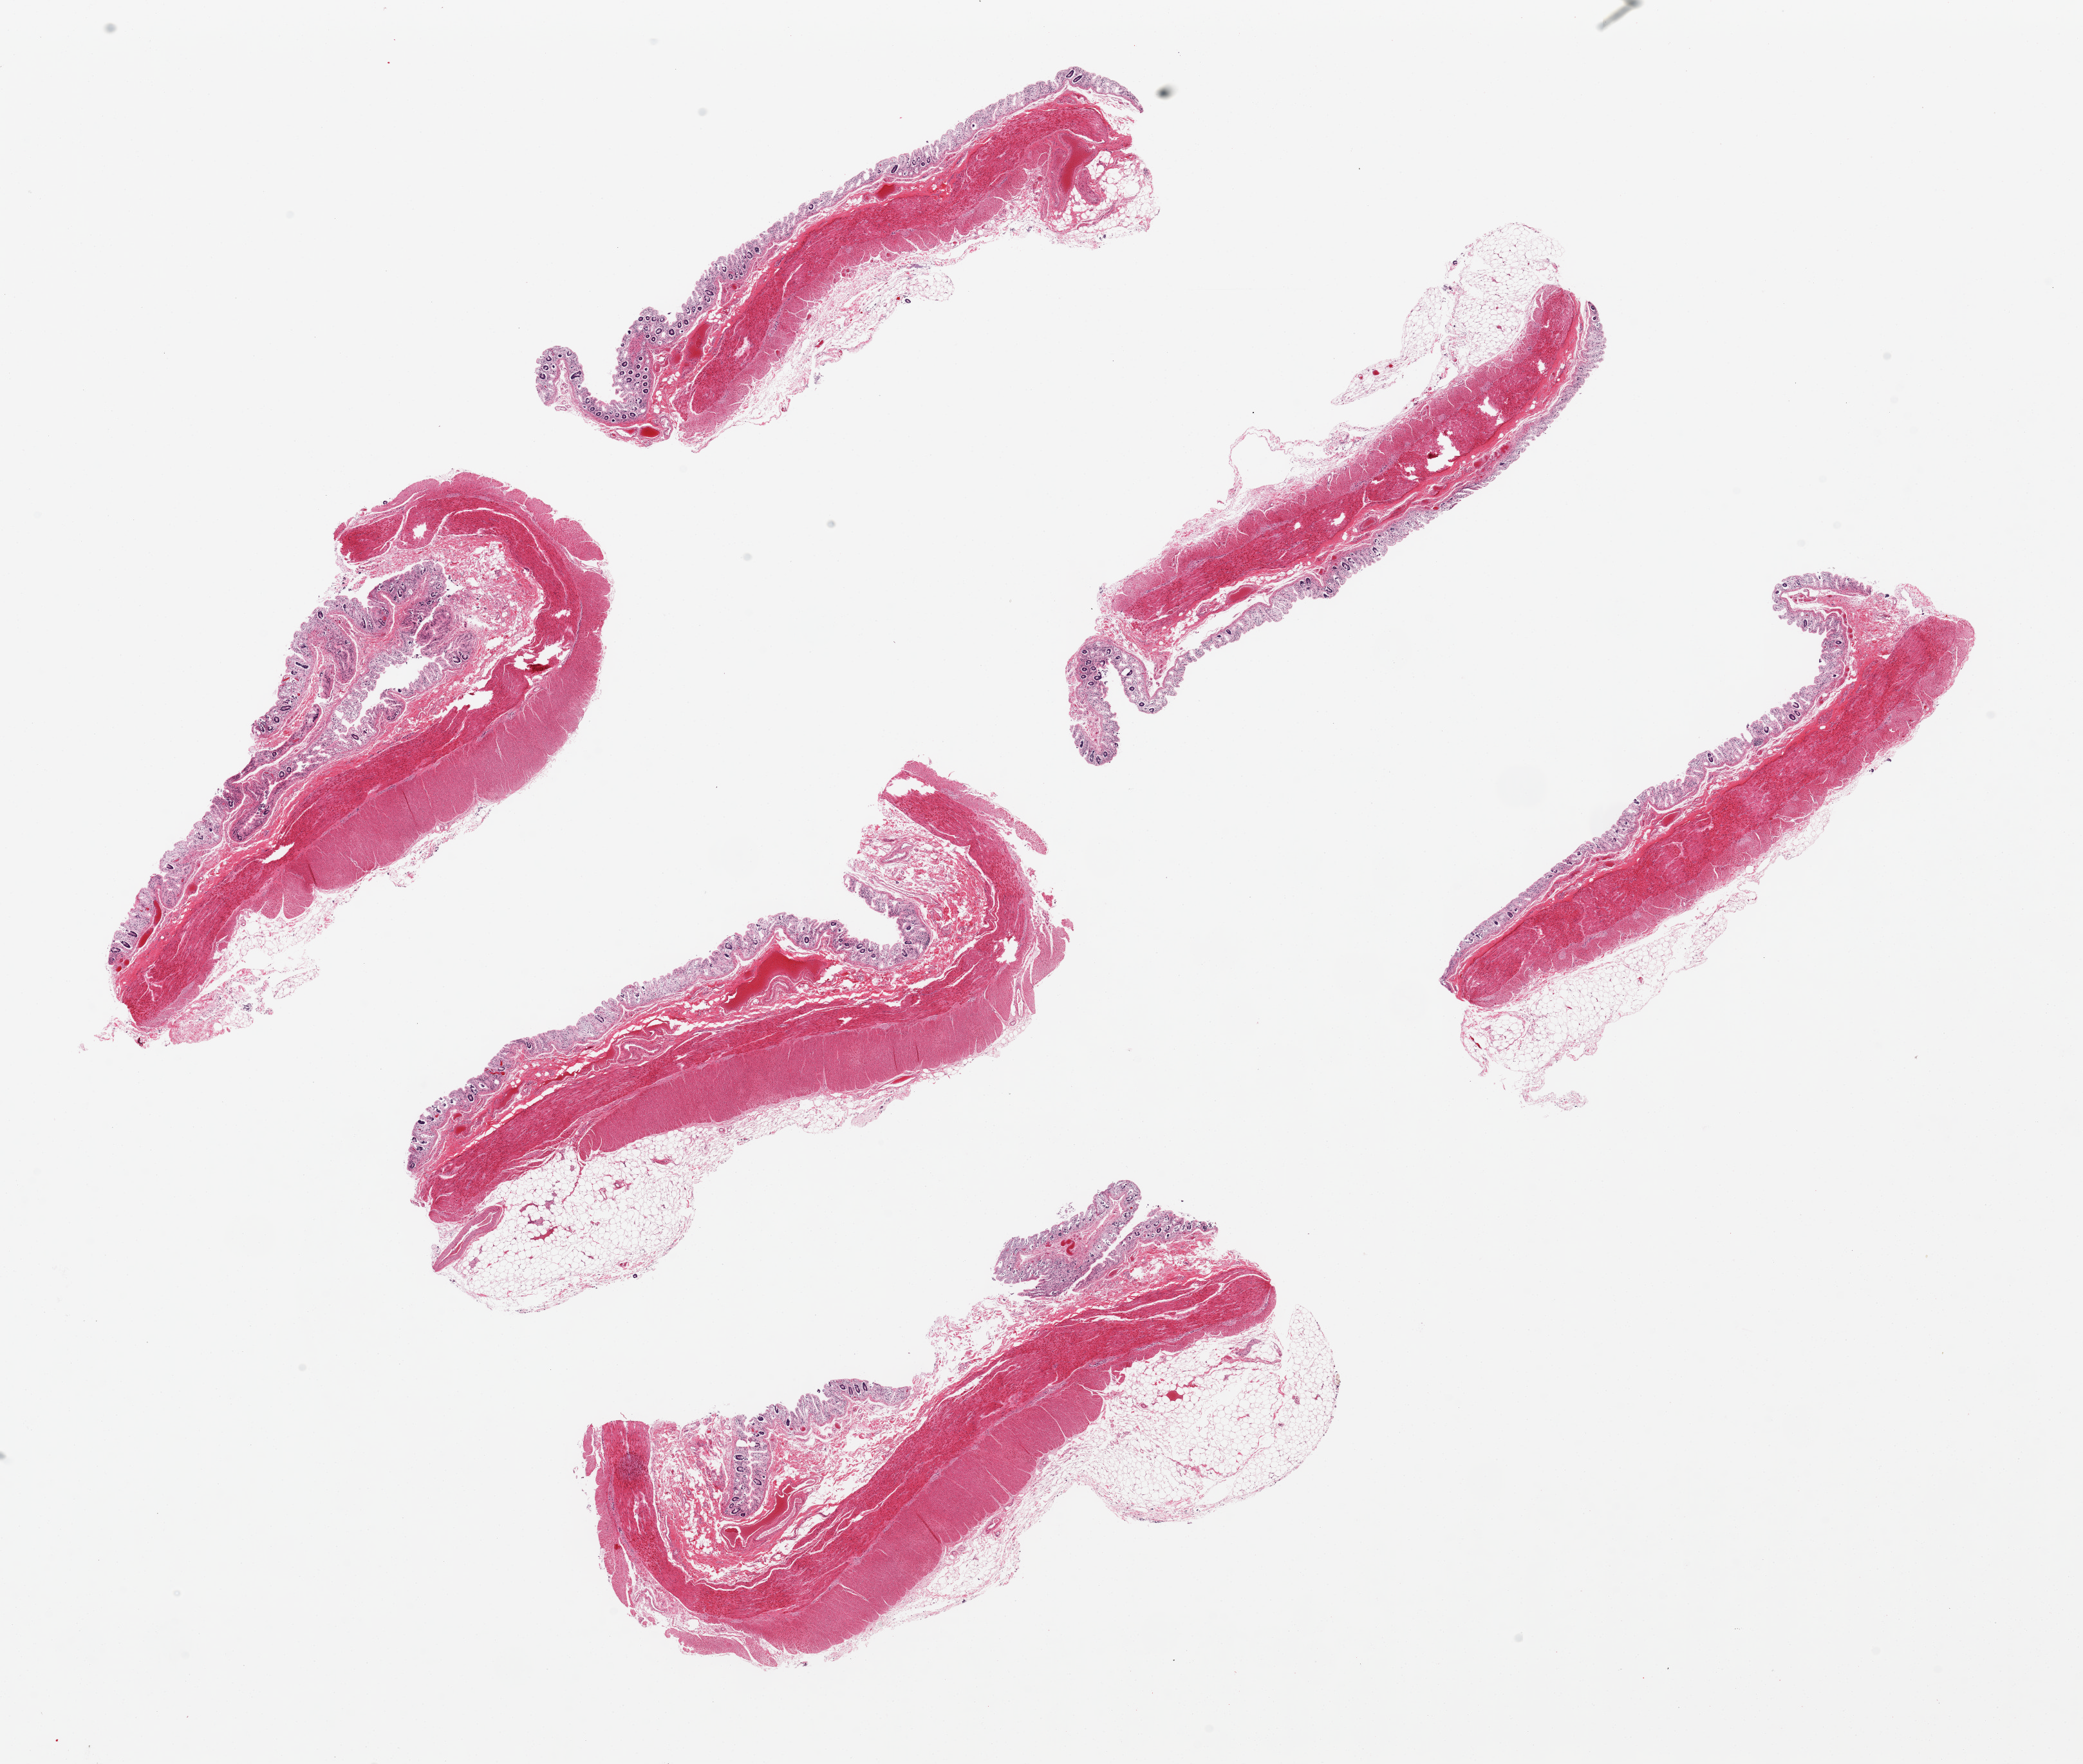
Whole-slide image, hematoxylin and eosin (H&E) stain — a low-resolution overview of the entire scanned area, about 25.6 x 21.7 mm (acquisition: 20x scan). PAXgene-fixed, paraffin-embedded tissue. Target tissue: transverse colon. Tissue donor sample. Donor sex: female.
Pathologist's review note for this sample: 6 pieces, ~7x1.5mm. Mucosa nearly totally autolyzed and/or sloughed.